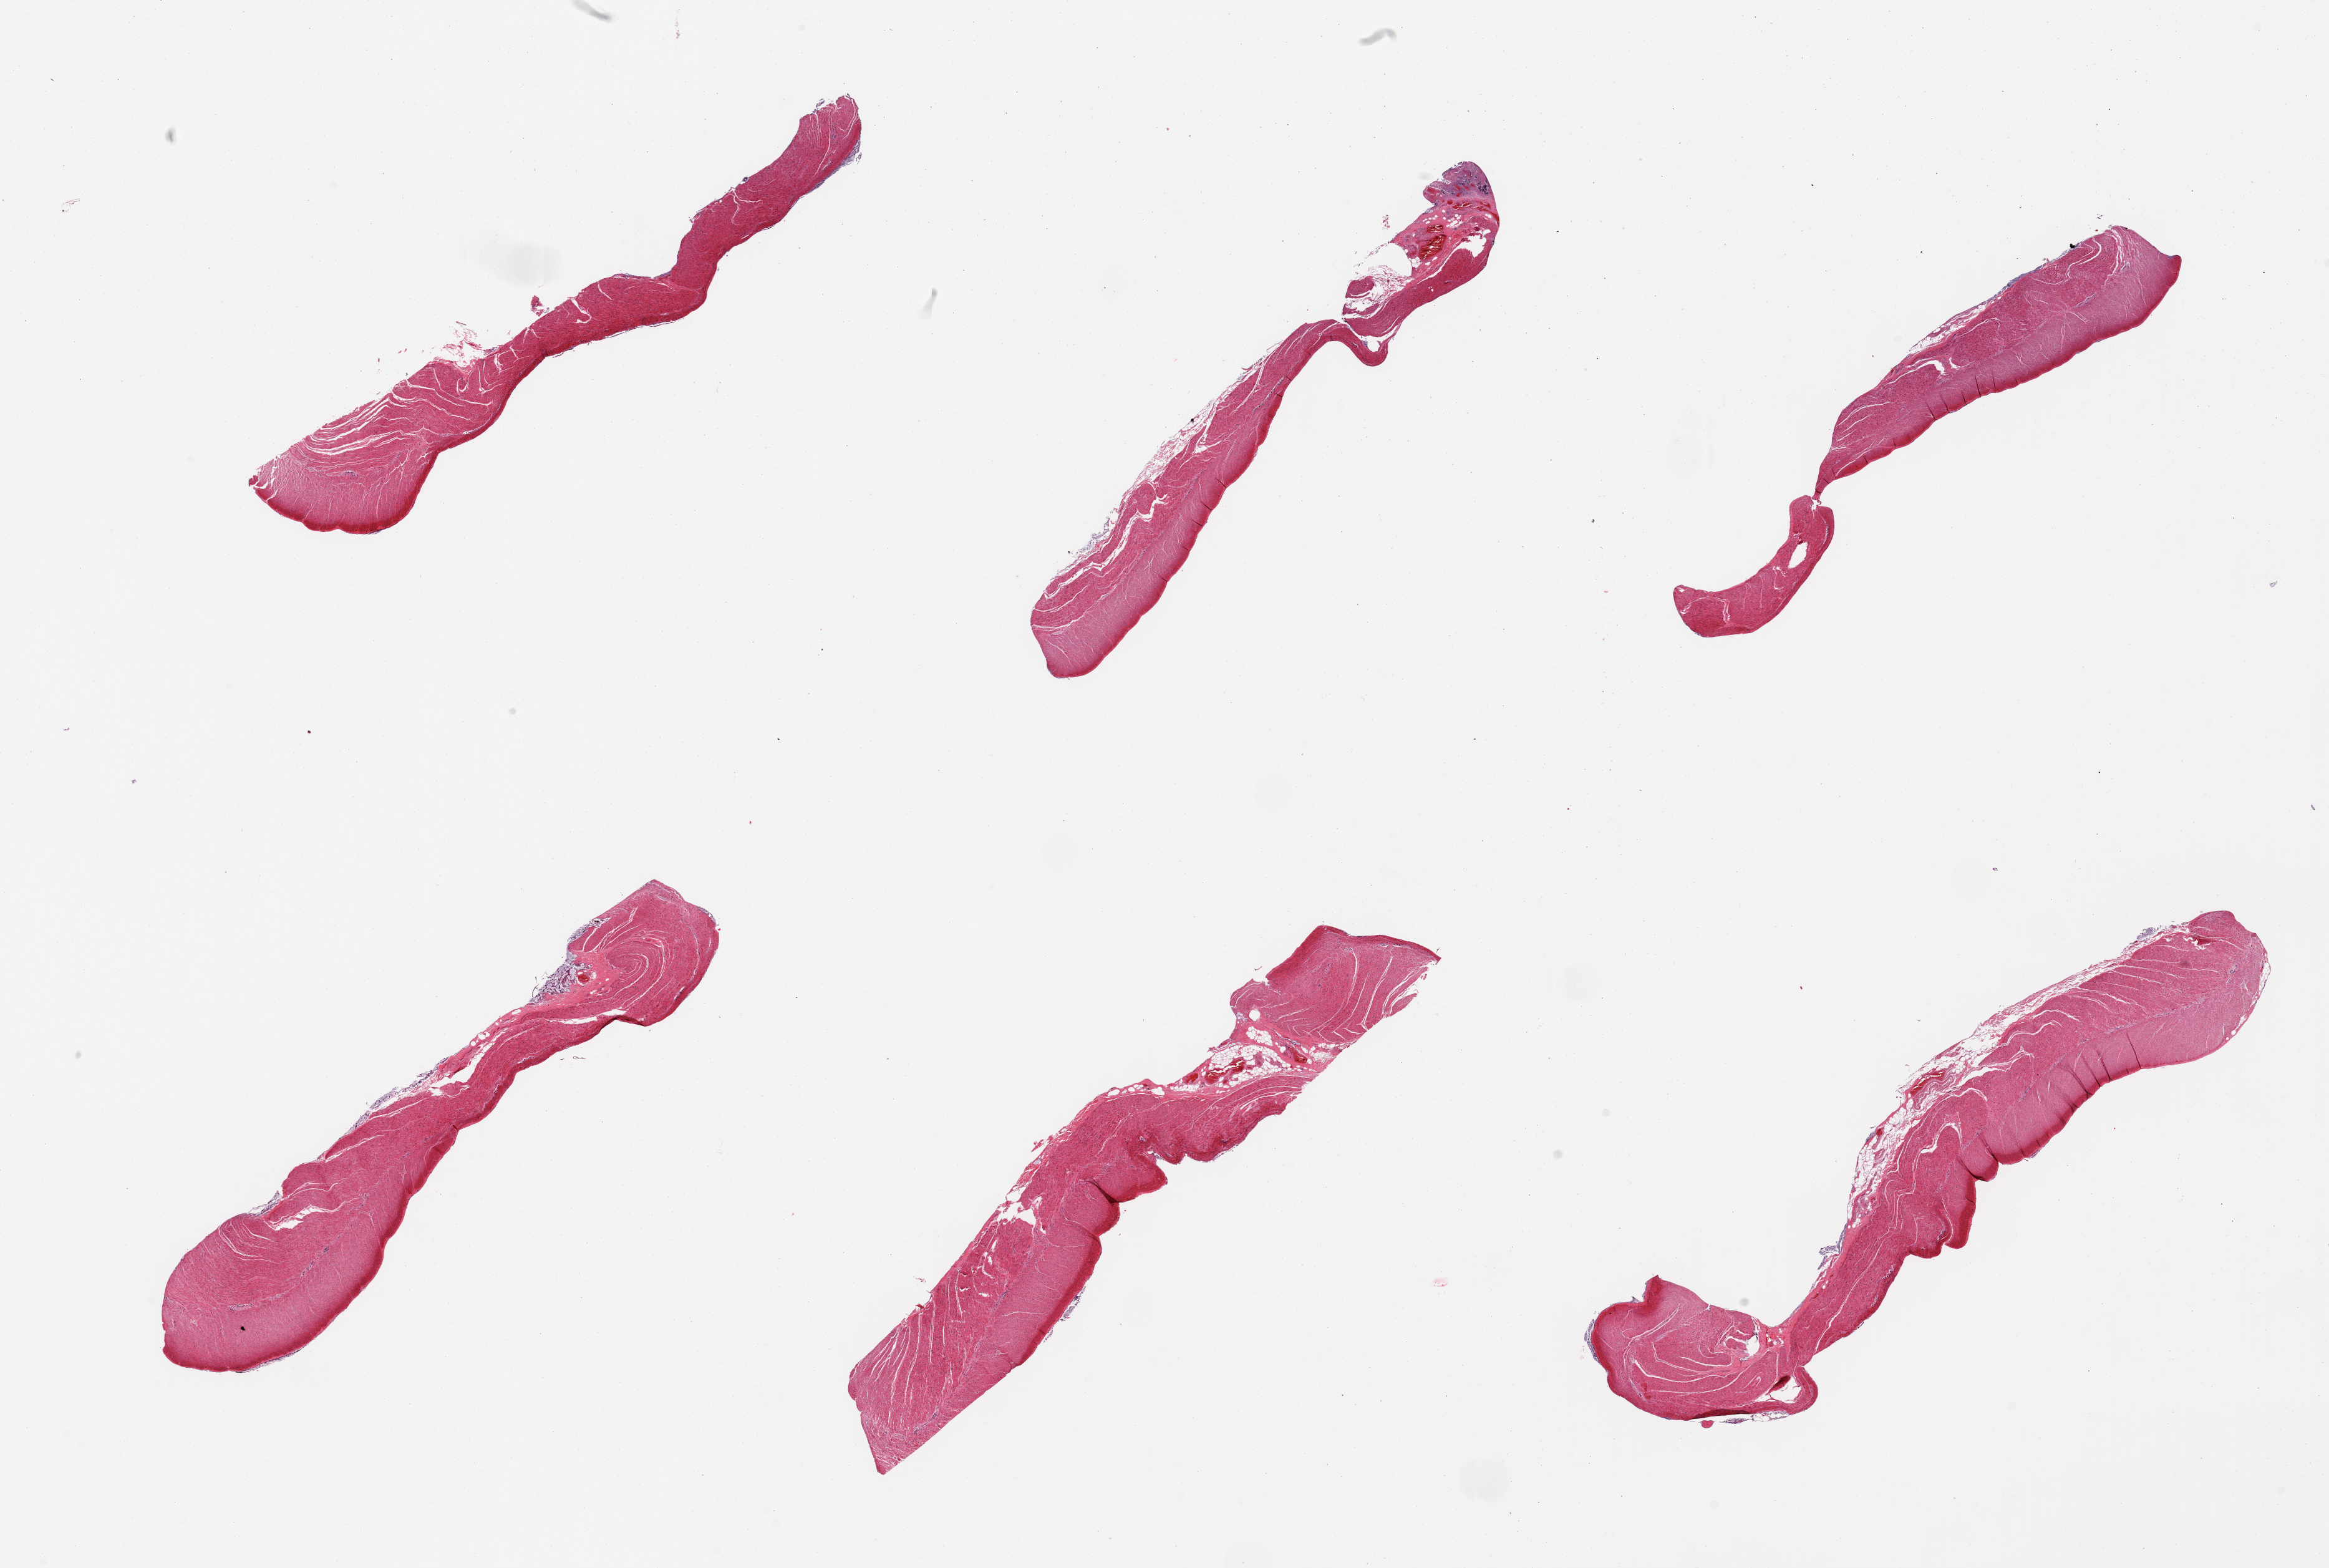
Hematoxylin and eosin (H&E) whole-slide image, a low-resolution overview of the entire scanned area, about 29.5 x 19.9 mm, PAXgene-fixed paraffin-embedded (PFPE) section, section of sigmoid colon (target tissue), tissue donor sample. Donor: male.
• reviewer comment on this tissue sample: 6 pieces, target muscularis, good specimen